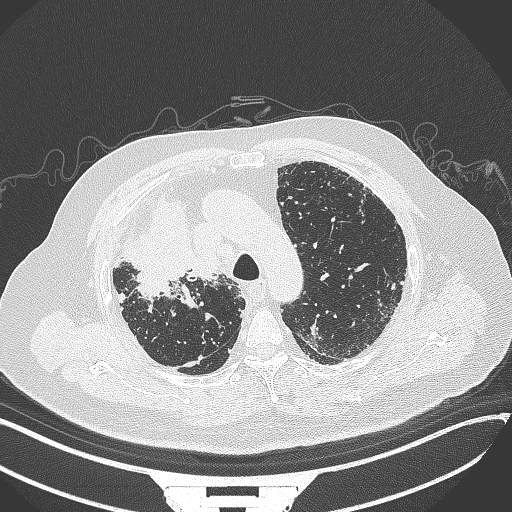
Chest CT, one axial slice; slice 265 of 384 in the series (ordered by position); lung window (W 1500 / L -600 HU); 1 mm slice thickness; 512 × 512 image matrix, field of view 400 × 400 mm. Patient: male, 69 years. From the clinical record (not read from this slice): clinical TNM (as recorded): T4 N3 M1.
Outlined on this slice (rectangle marked by the reading radiologist):
- lung tumour (recorded histology: adenocarcinoma): bounding box (x1, y1, x2, y2) in pixels: (119, 193, 213, 303)